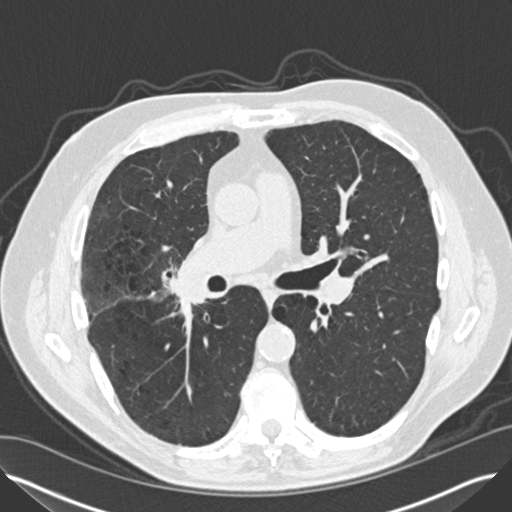
Low-dose screening chest CT, one axial slice. Slice 80 of 149 in the series (ordered by position). 120 kVp. Lung window (W 1500 / L -600 HU). 2 mm slice thickness. 512 × 512 image matrix, field of view 370 × 370 mm.
Outlined on this slice (outlined manually by an expert reader):
- lesion 2 (tumor, hilum of right lung): box from (x=174, y=266) to (x=208, y=301) px